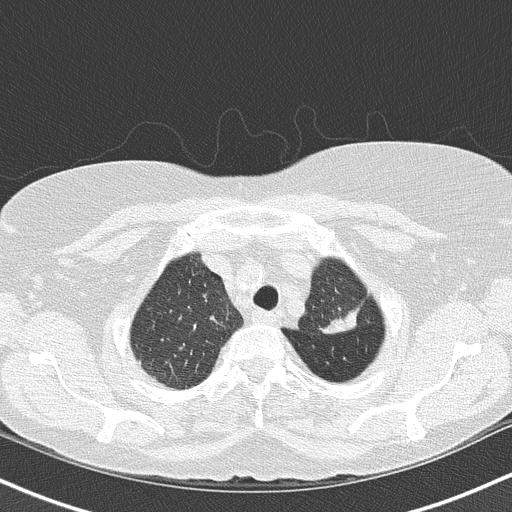
Low-dose screening chest CT, one axial slice. Slice 128 of 147 in the series (ordered by position). Lung window (W 1500 / L -600 HU). 2 mm slice thickness. 512 × 512 image matrix, field of view 320 × 320 mm.
Outlined on this slice (manually delineated by an expert):
- lesion 1 (tumor, upper lobe of left lung): bounding box <323,311,357,334> (left, top, right, bottom; pixels)